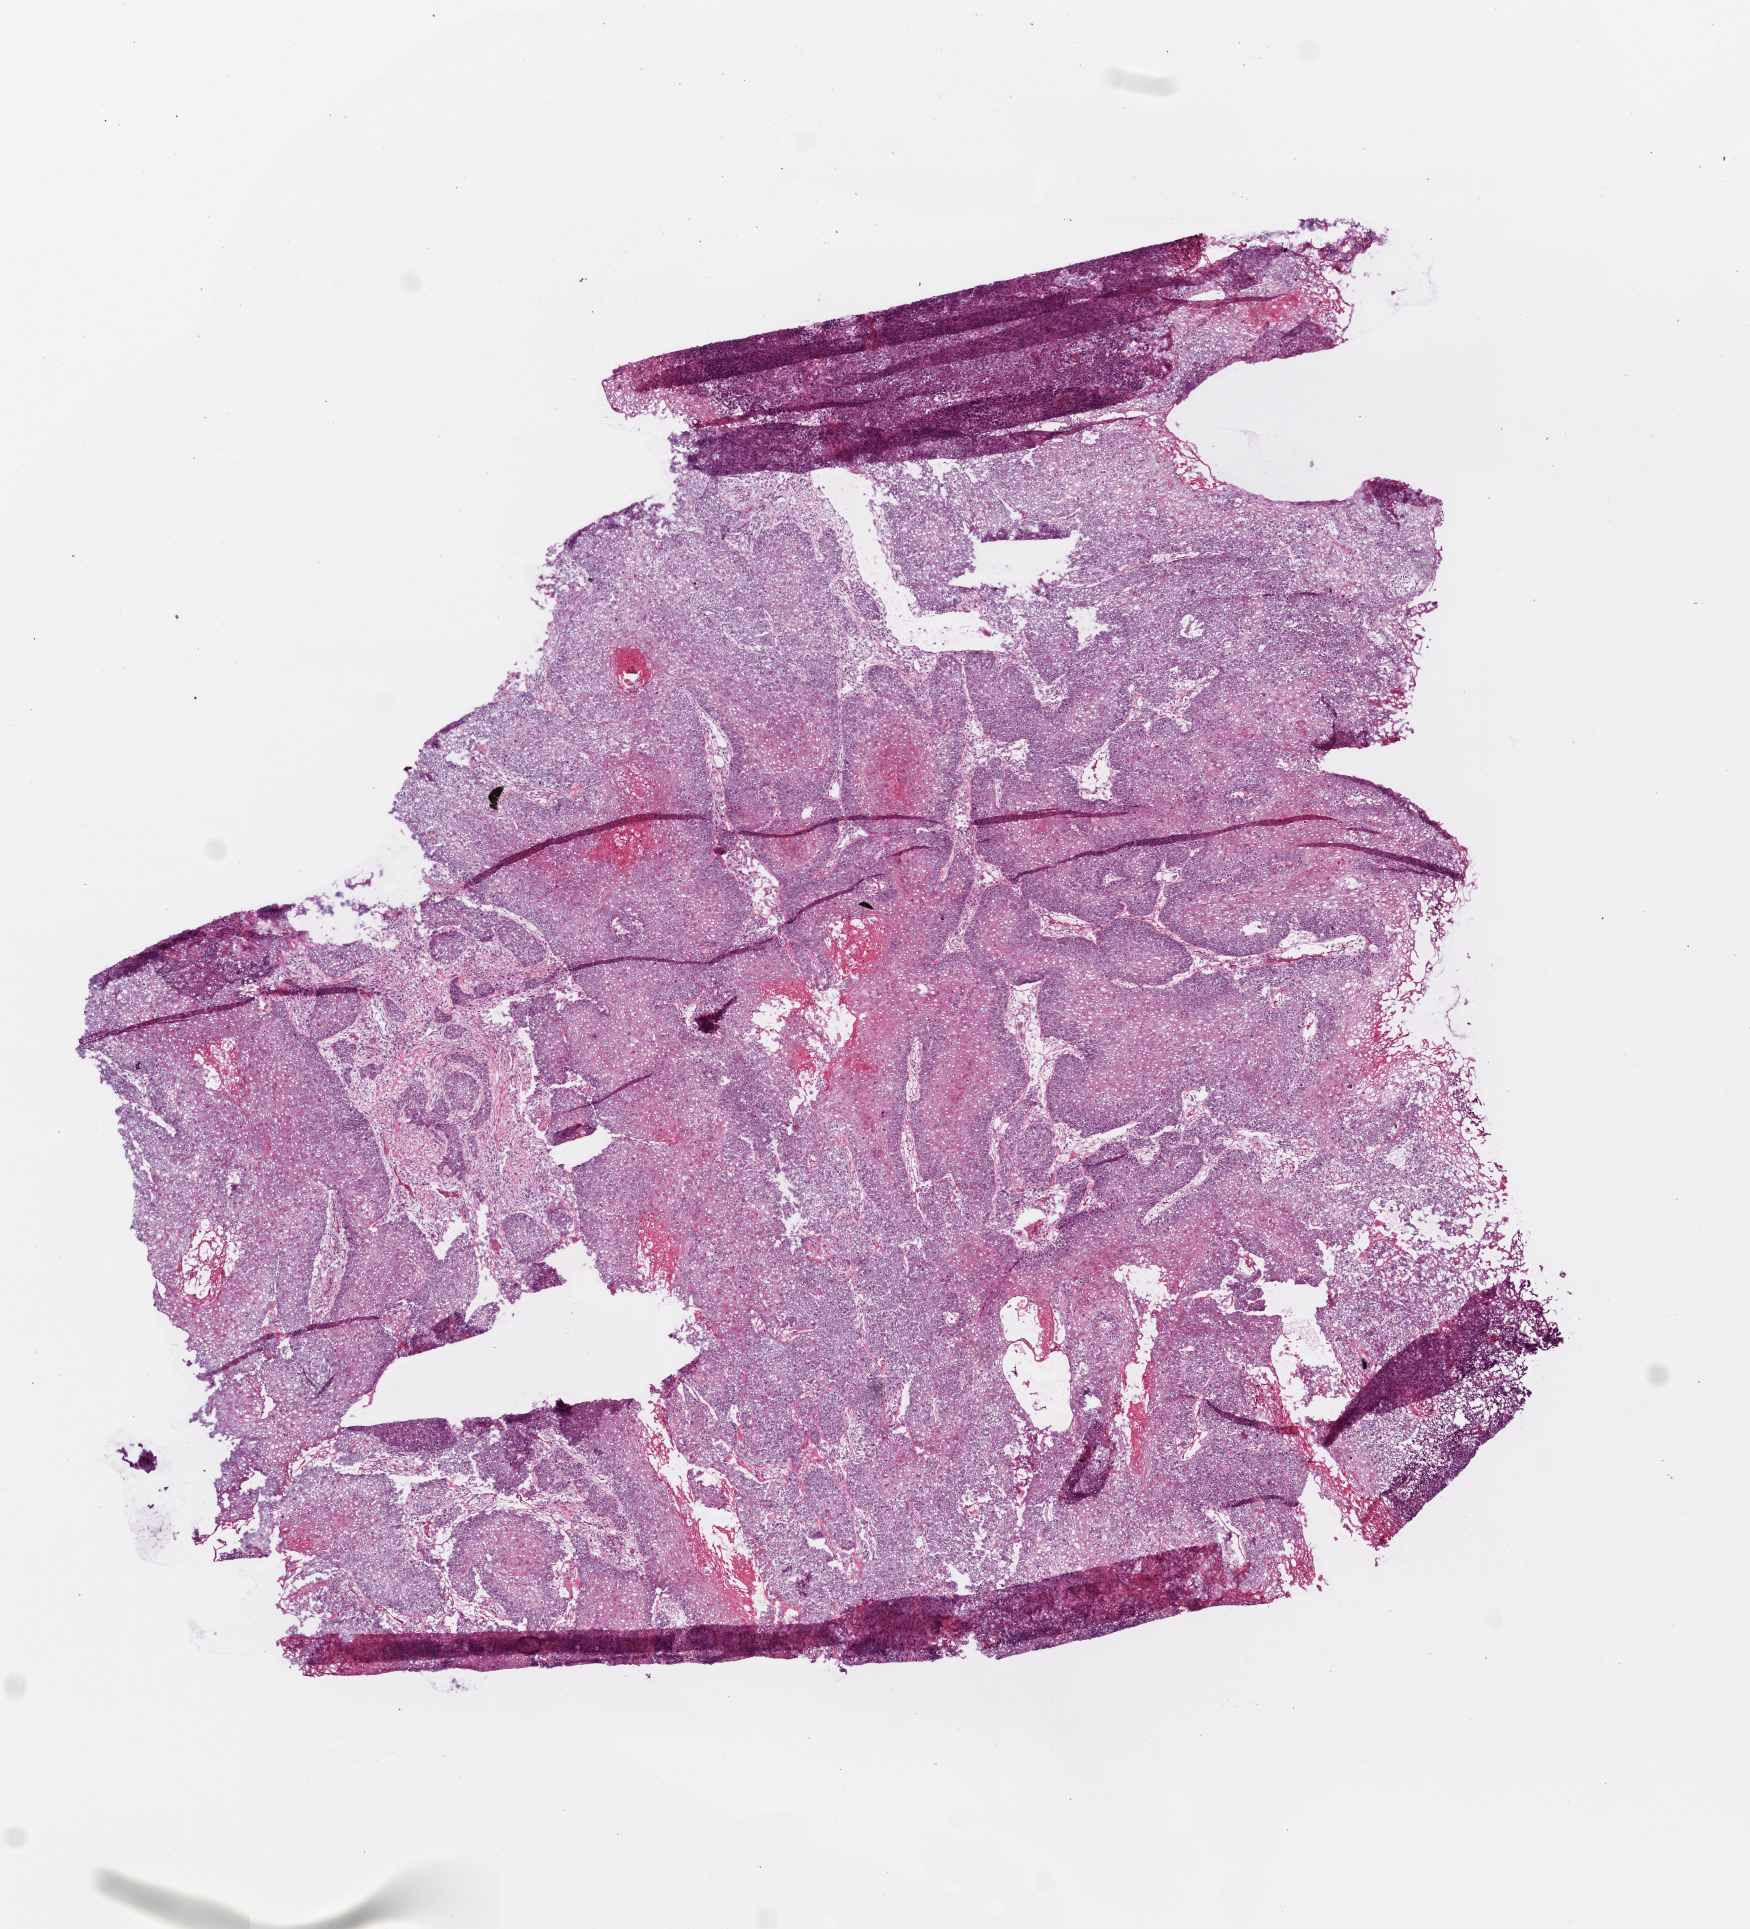
Whole-slide histology image, Hematoxylin and eosin (H&E) stained — shown as a low-resolution overview of the whole scanned area (about 7.0 x 7.7 mm, acquisition: 20x scan). Frozen section from the top of the tissue portion. Primary tumour sample from the head and neck. Male, age 39 years at initial diagnosis. Histologic grade: G2 (moderately differentiated). Slide review estimates, as recorded: tumour cells 95%, tumour nuclei 90%, normal cells 0%, stromal cells 3%, necrosis 2%.
* pathologic diagnosis: Squamous cell carcinoma, NOS (larynx, NOS)